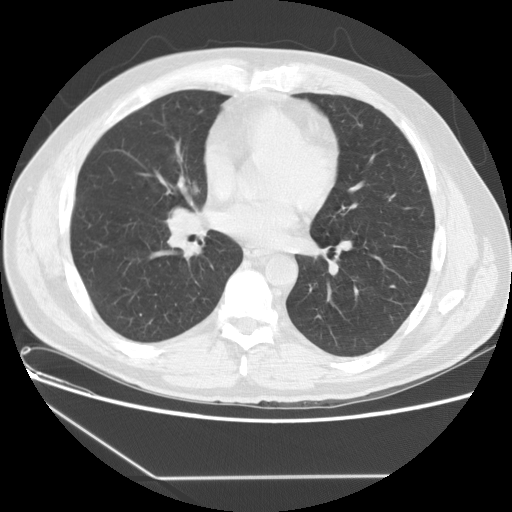
Low-dose screening chest CT, one axial slice; position 69 of 154 along the scan axis; reconstruction kernel STANDARD; lung window (W 1500 / L -600 HU); 2.5 mm slice thickness; 512 × 512 image matrix, field of view 370 × 370 mm.
Structures marked on this image (outlined manually by an expert reader):
- lesion 1 (tumor, middle lobe of right lung): box from (x=171, y=209) to (x=196, y=233) px